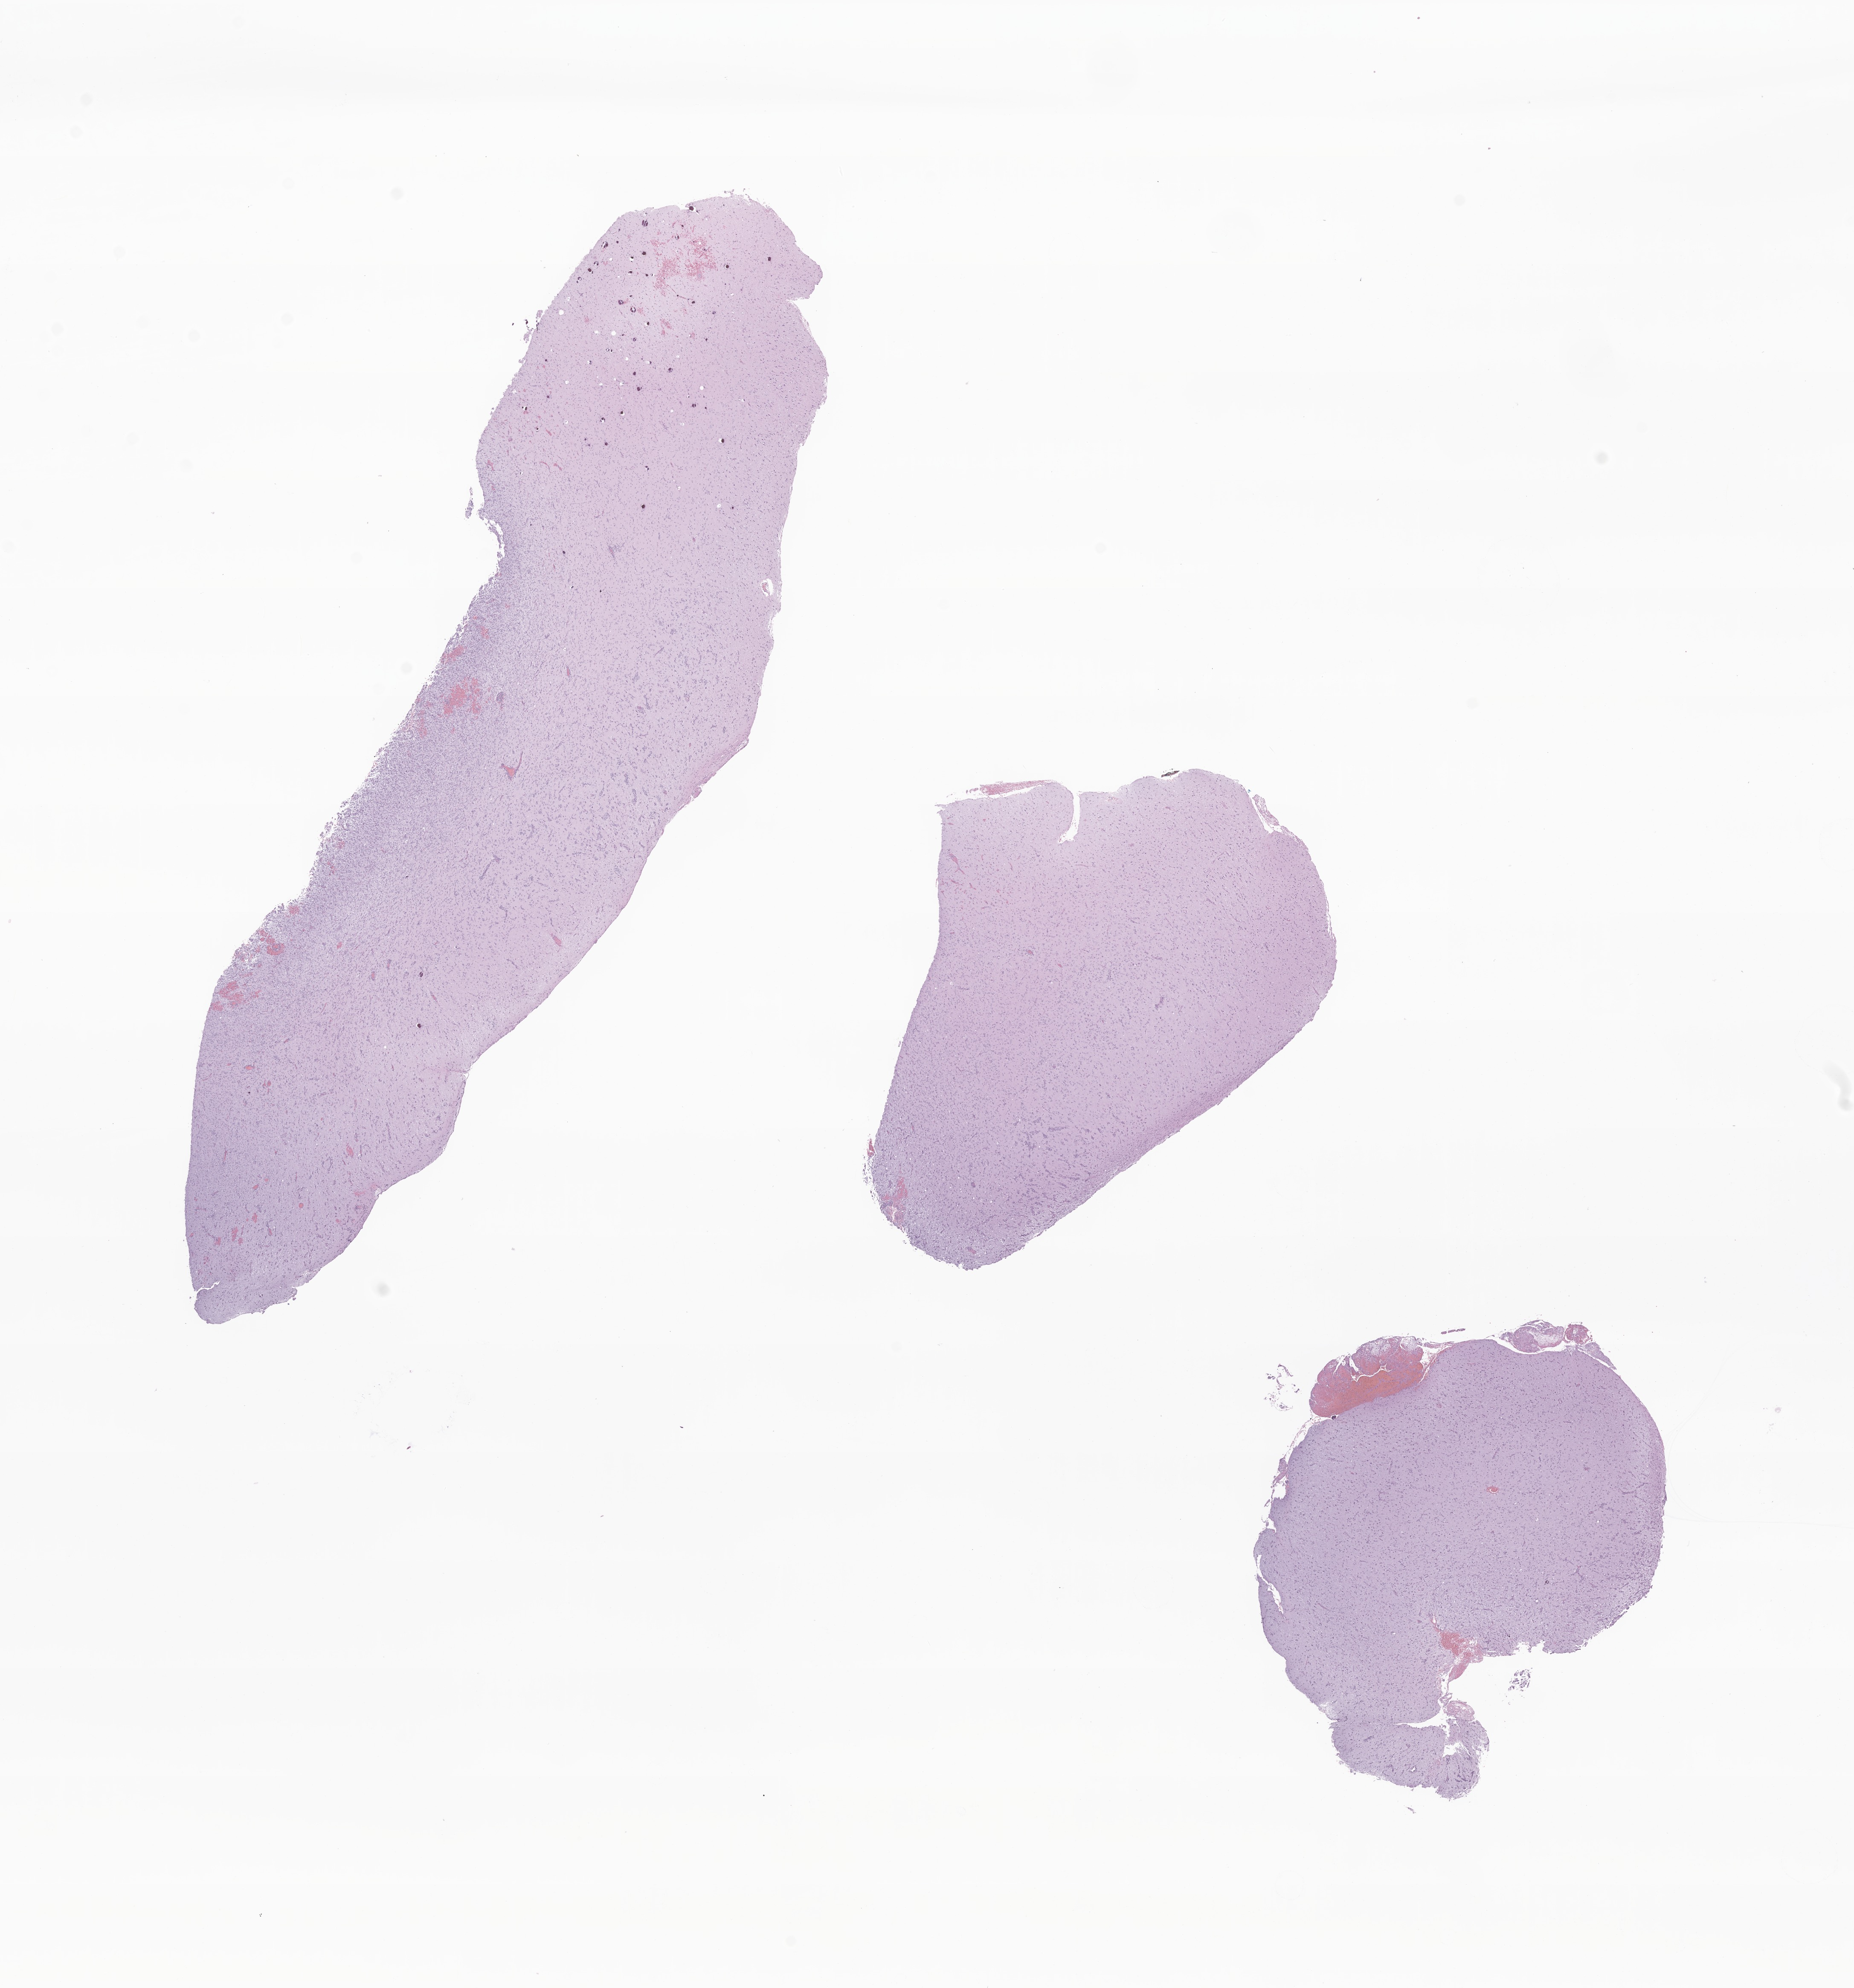
Whole-slide image, H&E stain of tumor tissue from the temporal lobe, whole scanned area (about 18.3 x 19.7 mm) shown as a low-resolution overview; formalin-fixed paraffin-embedded section. Patient male; age 43 months.
Diagnosis (ICD-O-3 morphology term): Pilocytic astrocytoma.